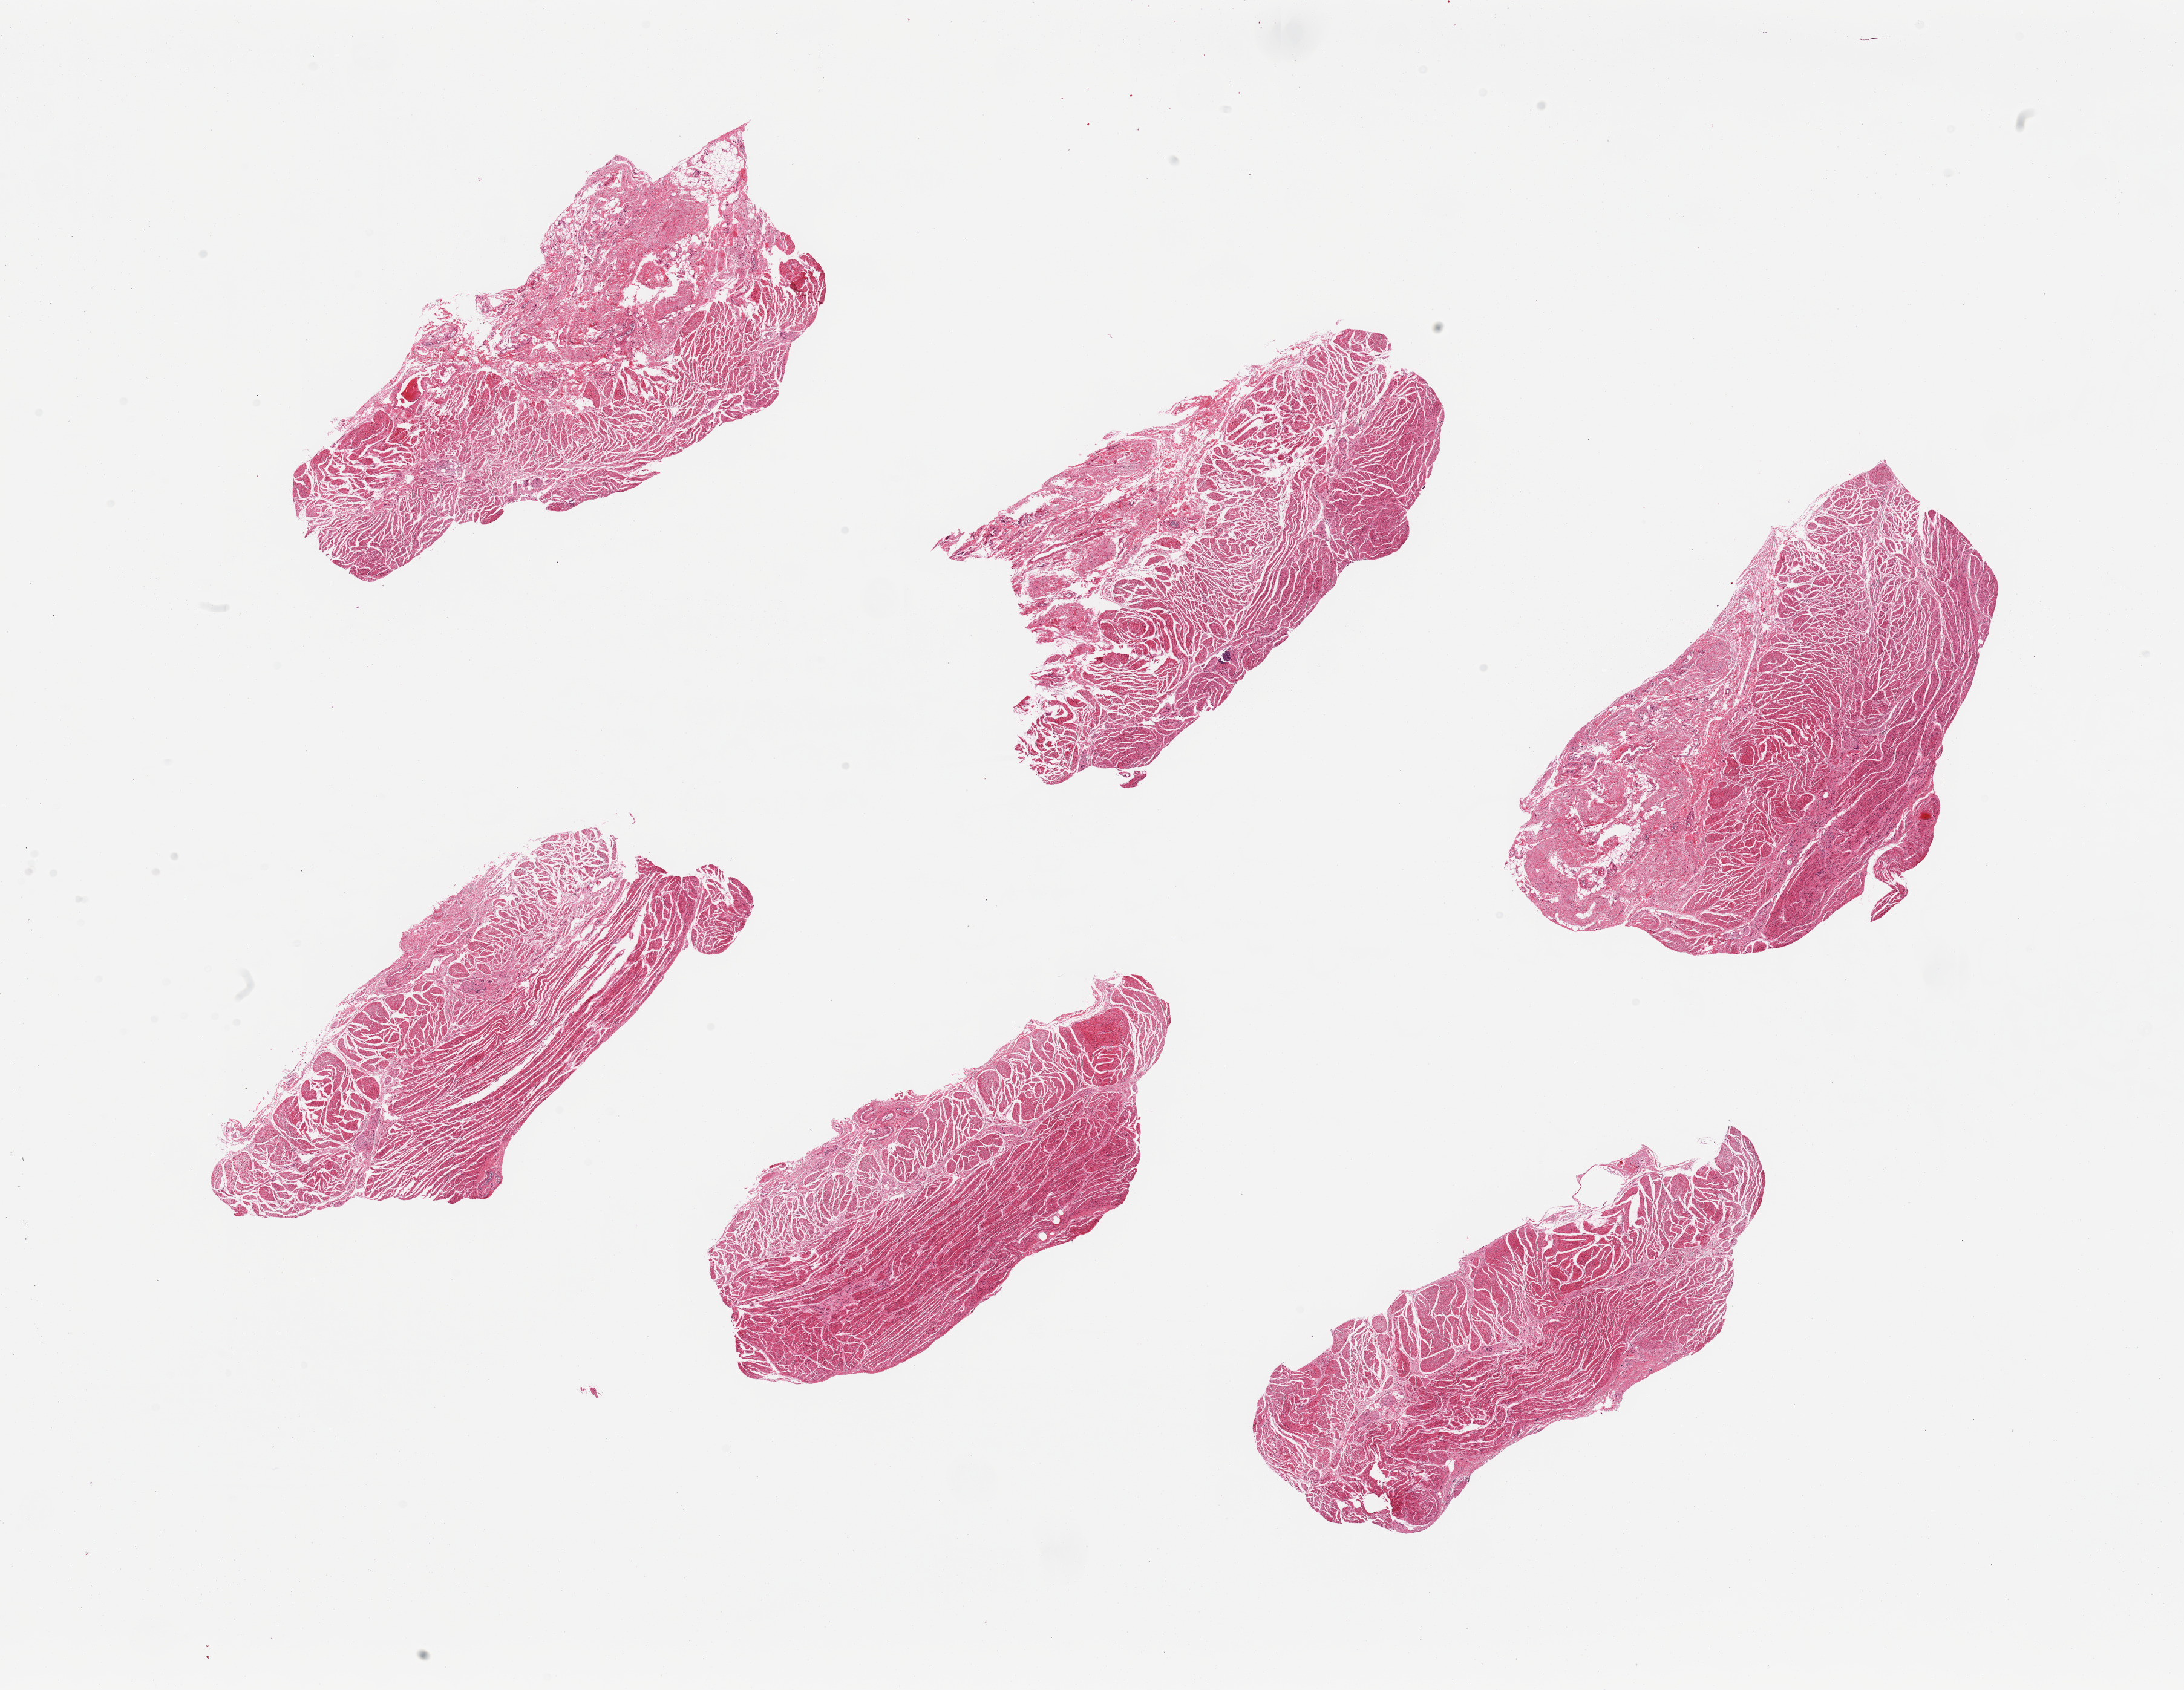
Digitized hematoxylin and eosin (H&E)-stained section, brightfield, low-resolution overview of the scanned area, about 28.5 x 22.1 mm (acquisition: 20x scan); PAXgene-fixed, paraffin-embedded tissue; sampled site (target tissue): gastroesophageal junction; donor tissue sample. Donor: female.
- review note (as recorded): 6 pieces; well trimmed muscle